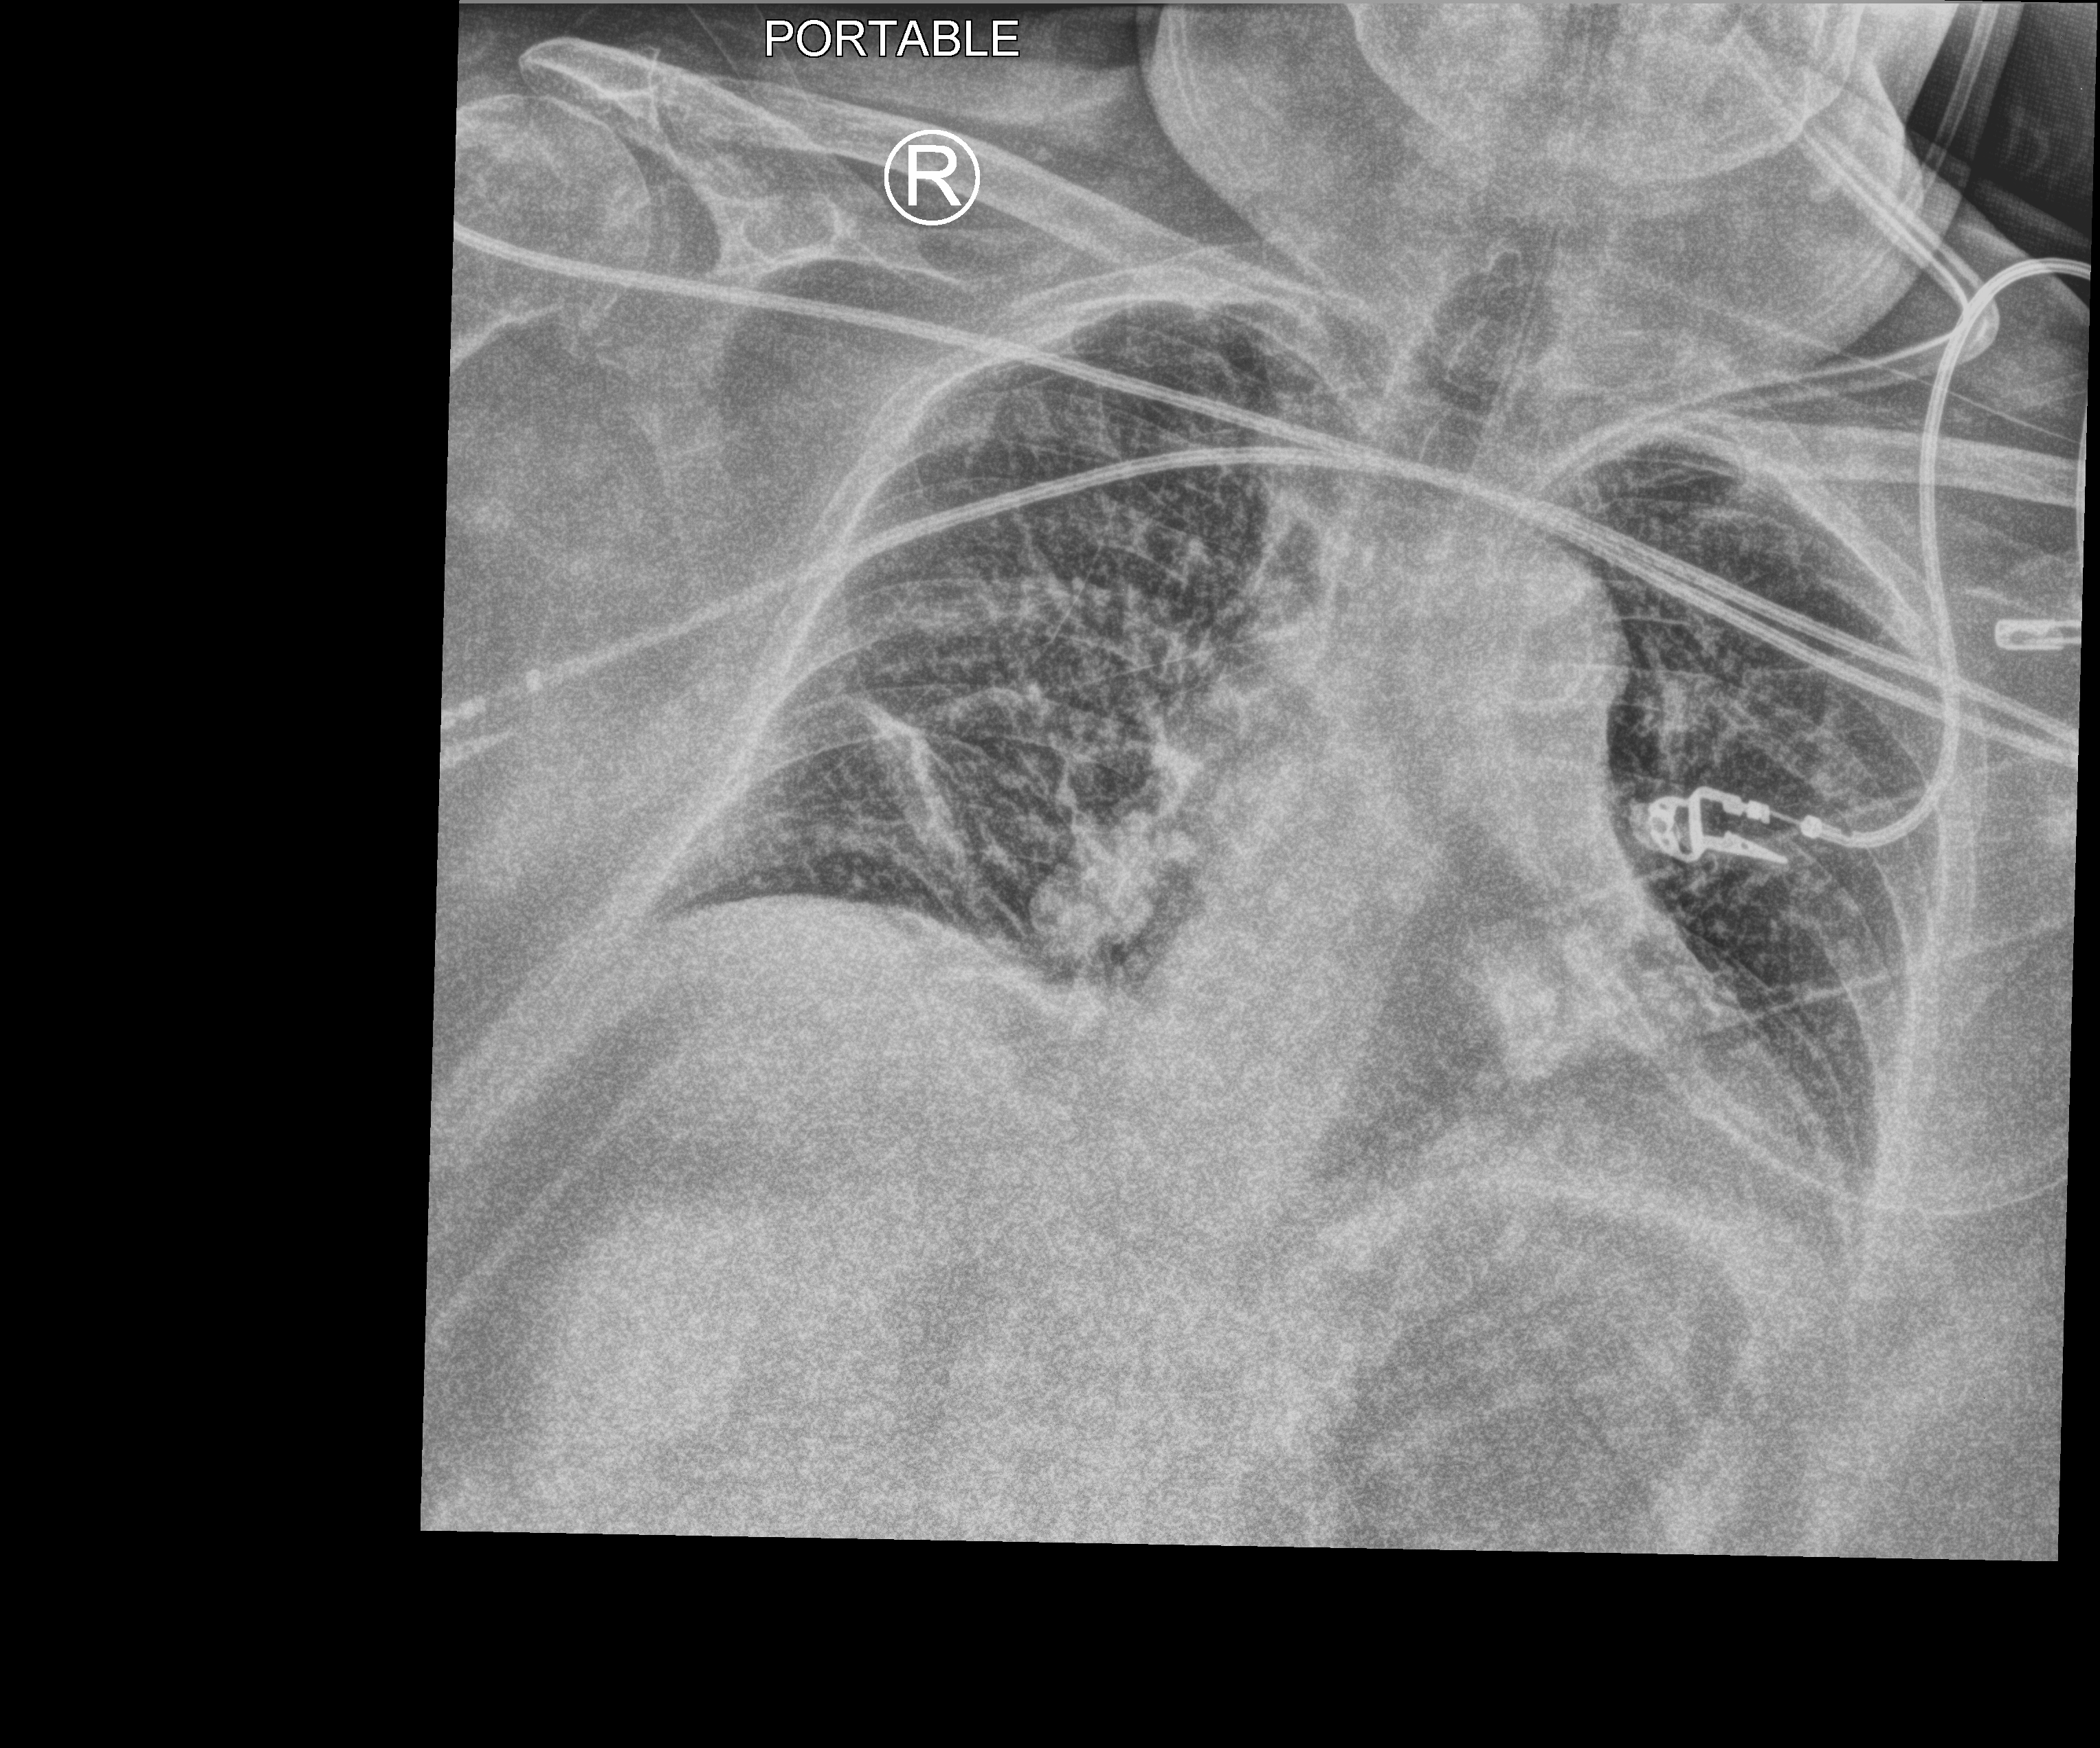
Bedside chest radiograph (computed radiography); anteroposterior (AP) projection. Patient hospitalised with COVID-19; female, aged 60–74 years.
From the hospital-stay record, not from the radiograph (when in the stay this image was taken is not recorded): admitted to intensive care during this hospital stay: yes; mechanically ventilated during this hospital stay: no.